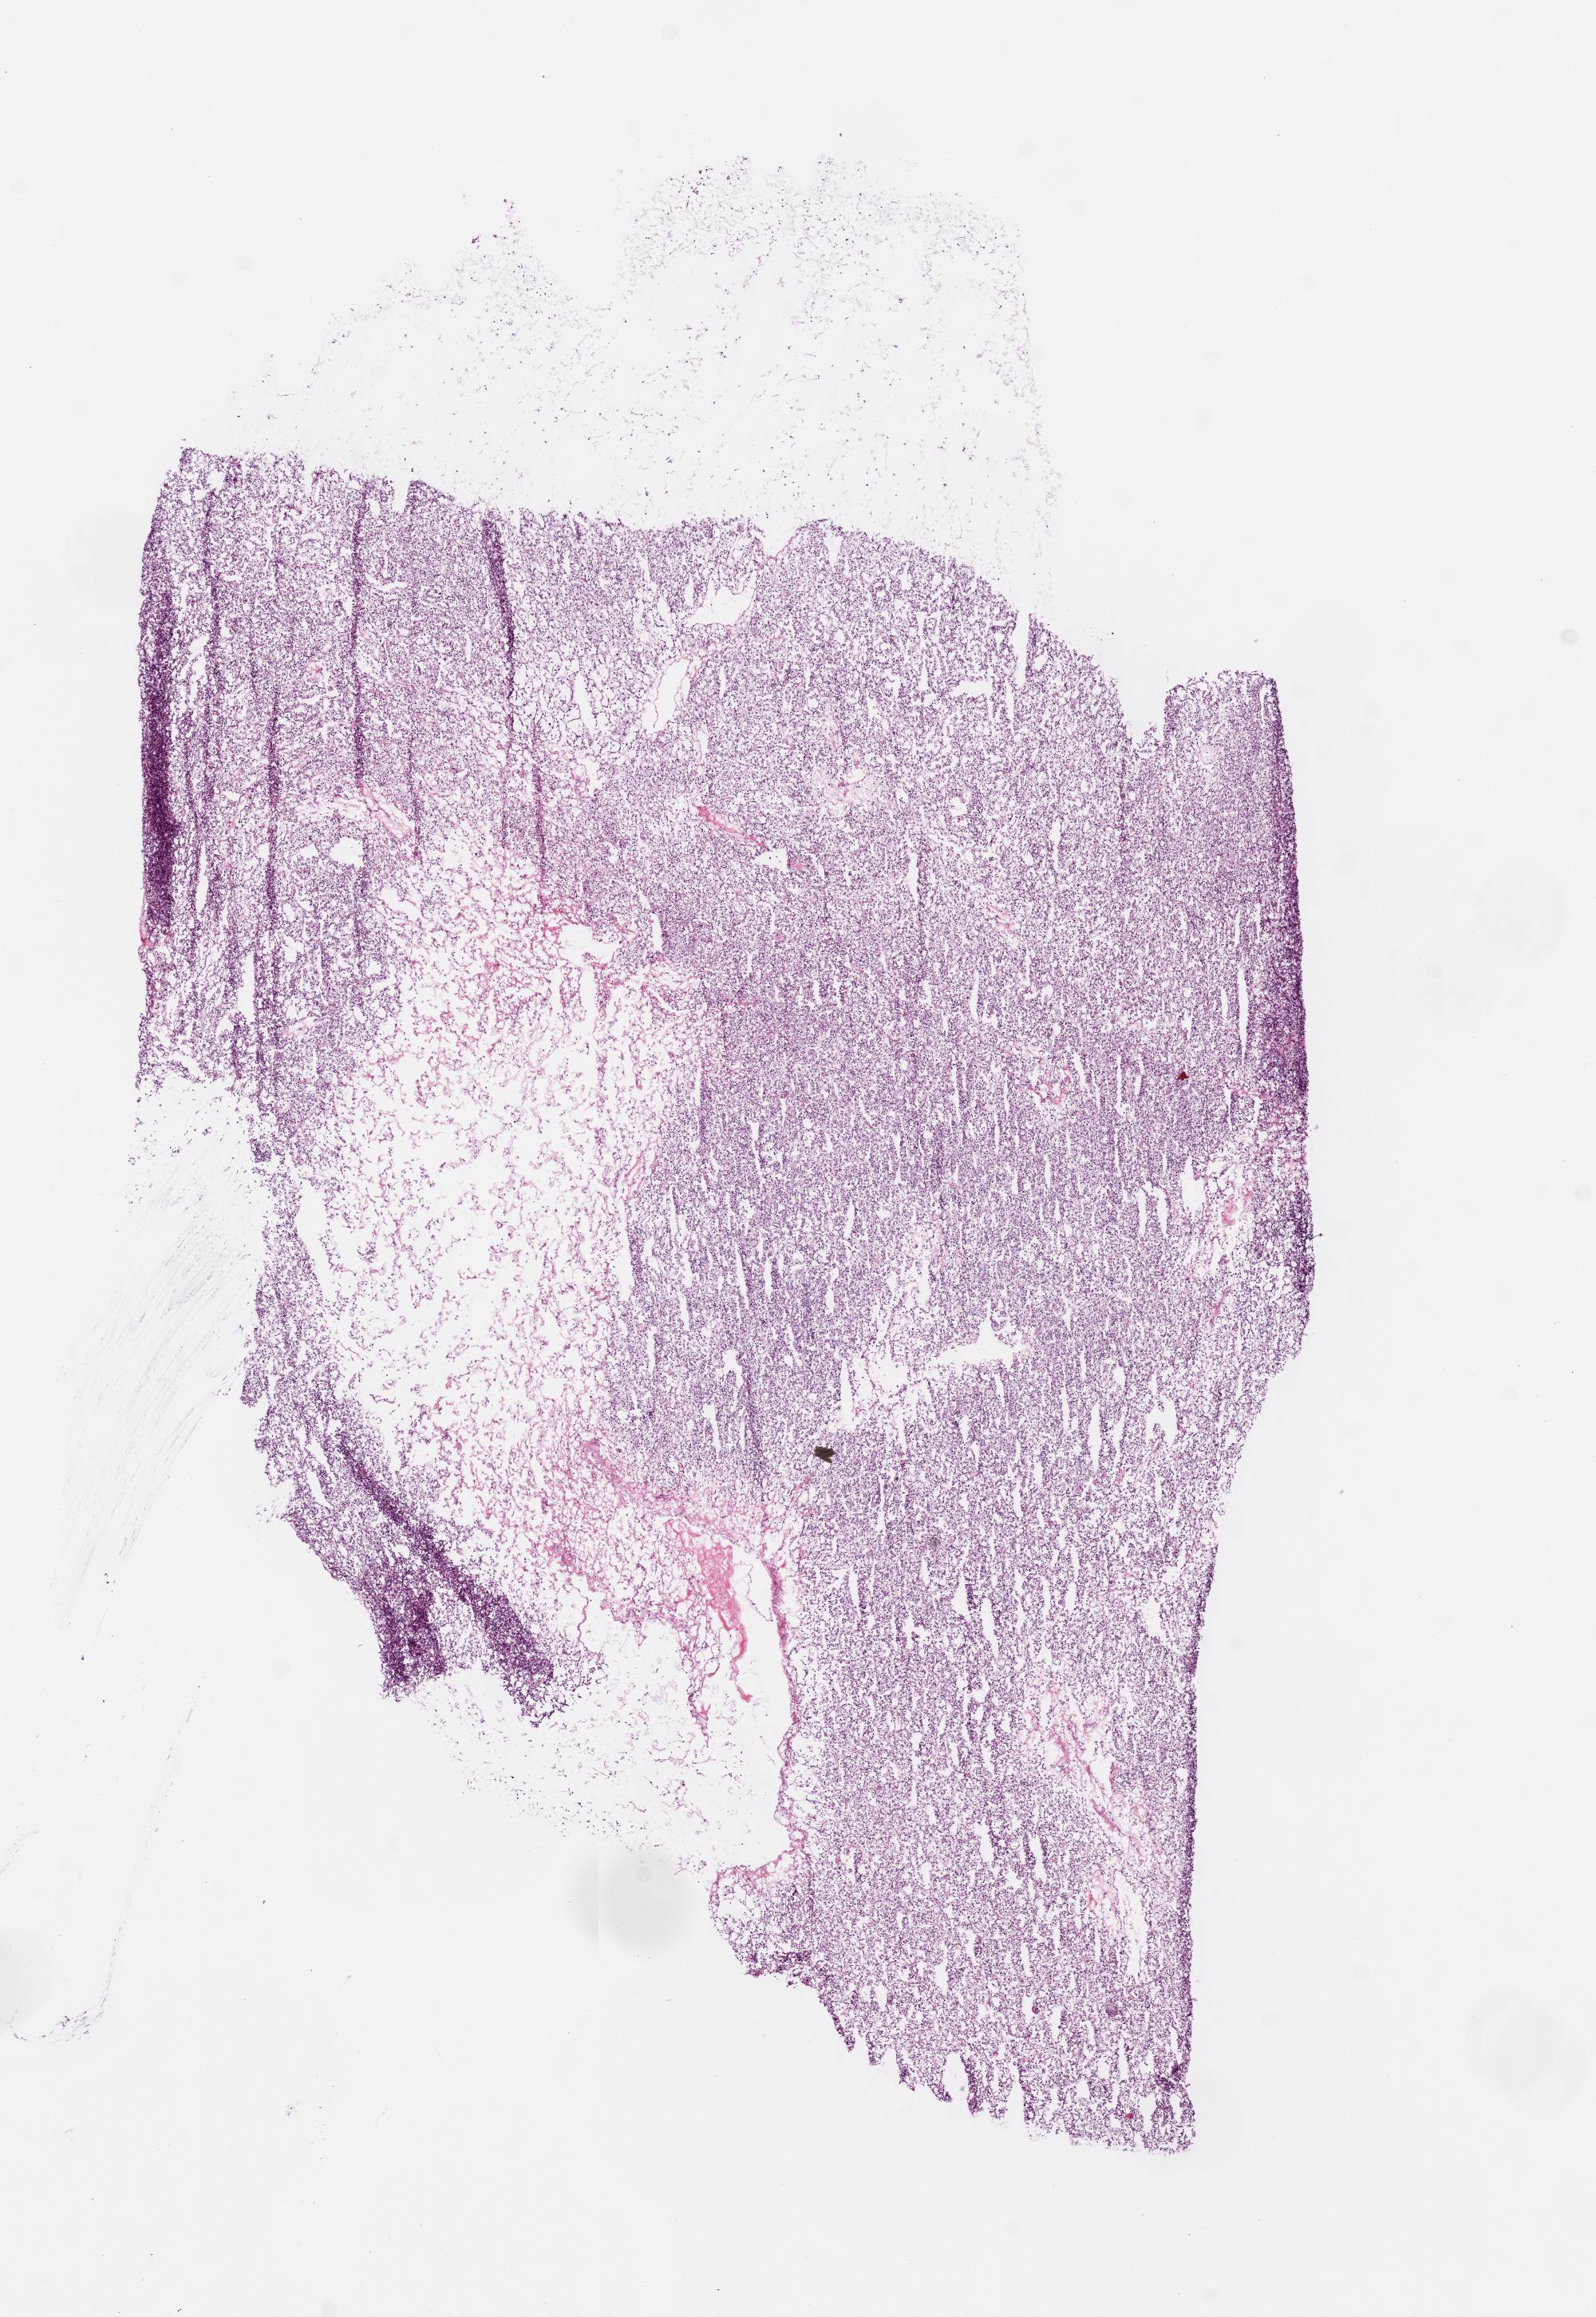
Digitized H&E tissue section (whole slide), whole scanned area (about 8.0 x 11.6 mm, slide scanned at 20x) shown as a low-resolution overview; frozen section from the bottom of the tissue portion; kidney, primary tumour sample. Patient: female, age at initial diagnosis 82 years. Histologic grade: G2 (moderately differentiated). Pathologist review of this section (percent, as recorded): tumour cells 80%, tumour nuclei 80%, normal cells 0%, stromal cells 20%, necrosis 0%.
* pathologic diagnosis: Clear cell adenocarcinoma, NOS
* AJCC pathologic stage: I
* laterality: left
* TNM: T1a N0 M0